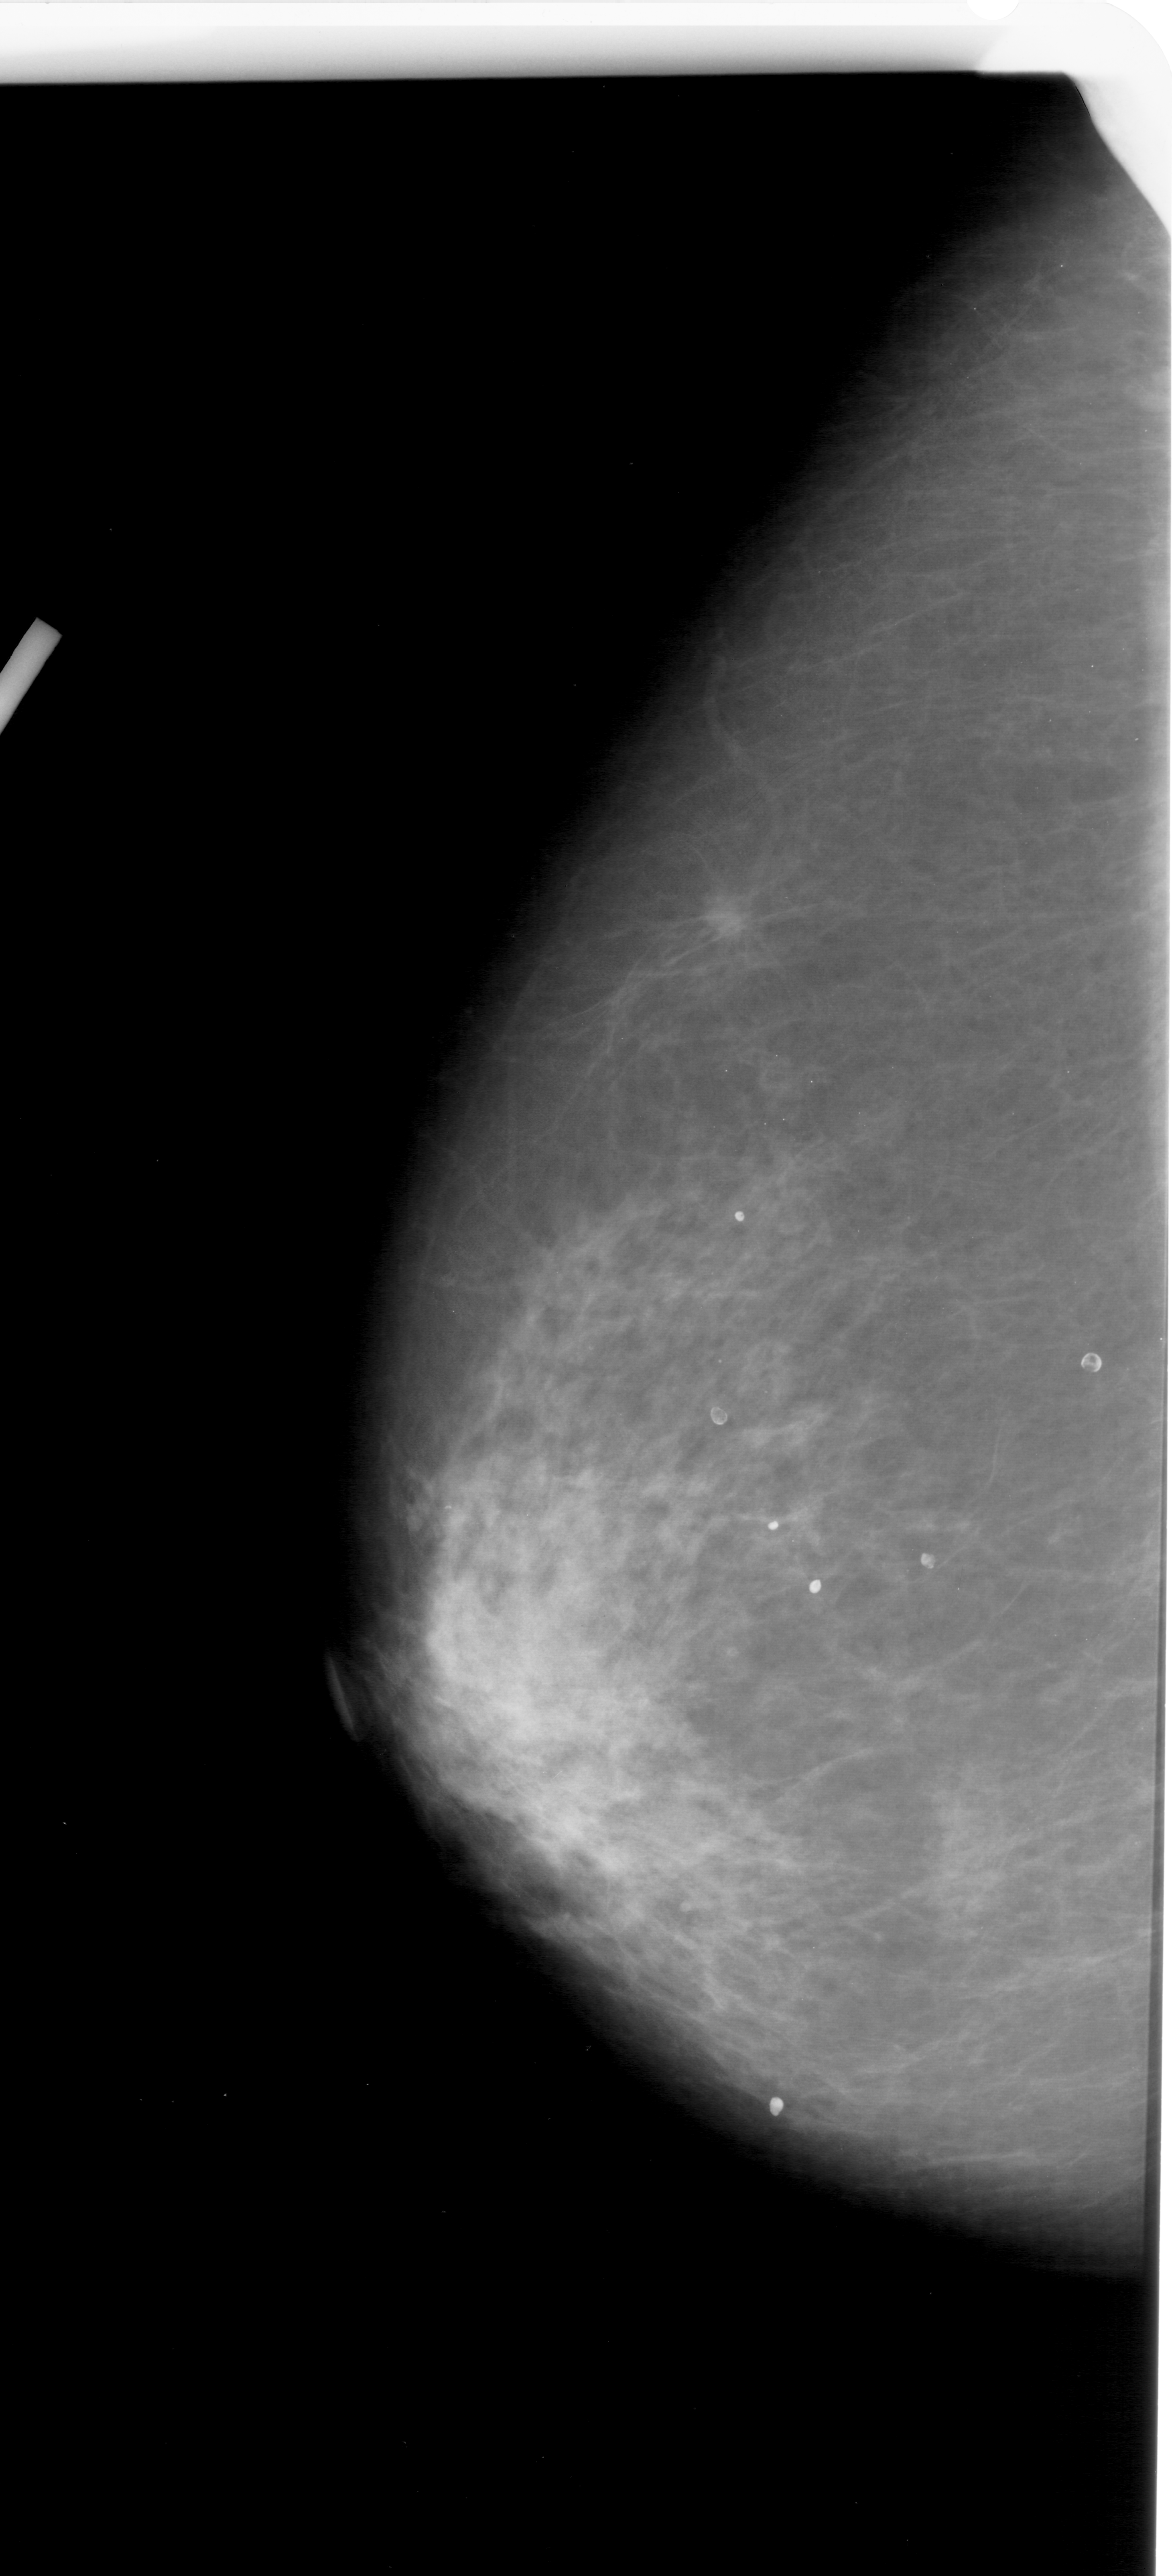
Digitized screen-film mammogram; left breast; craniocaudal (CC) view; breast composition: heterogeneously dense (BI-RADS density category 3 of 4).
Finding: mass, shape oval, margins ill defined; BI-RADS assessment category 4; pathology (as recorded): malignant.